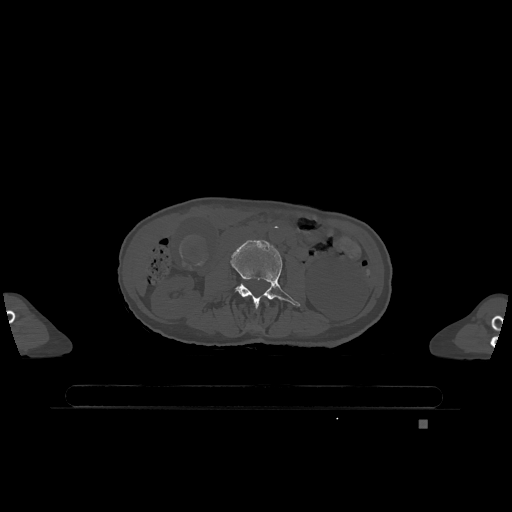
CT including the spine, one axial slice. Slice 358 of 1317 in the series (ordered by position). Bone window (W 1800 / L 400 HU). 512 × 512 image matrix, field of view 500 × 500 mm. Female patient, age 74 years. Case-level facts recorded for this patient, not image findings: primary cancer: lung; vertebrae with lytic lesions (as recorded): T1, T4, T5, T6, L4, L5.
Annotated regions visible in this slice (semi-automatic segmentation, software-assisted and operator-edited):
- L2 vertebra: bounding box (x1, y1, x2, y2) in pixels: (267, 303, 269, 305)
- L3 vertebra: (231, 240, 300, 308)